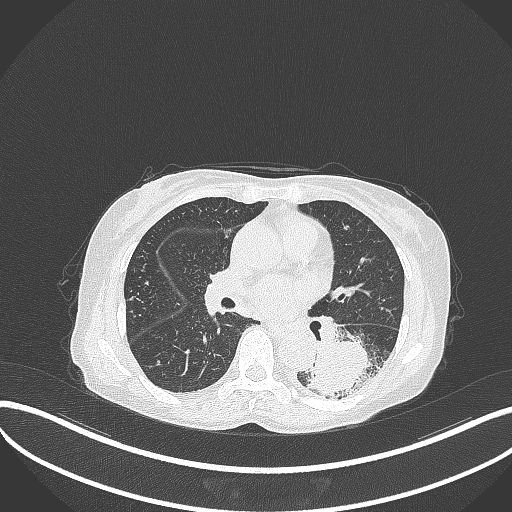
Chest CT, one axial slice; position 162 of 370 along the scan axis; reconstruction kernel B70f; 120 kVp; lung window (W 1500 / L -600 HU); 1 mm slice thickness; 512 × 512 image matrix, field of view 400 × 400 mm. Female patient, age 78 years. Case-level facts recorded for this patient, not image findings: clinical TNM (as recorded): T3 N0 M1.
Structures marked on this image (rectangle marked by the reading radiologist):
- lung tumour (recorded histology: squamous cell carcinoma): bounding box (x1, y1, x2, y2) in pixels: (308, 333, 385, 401)